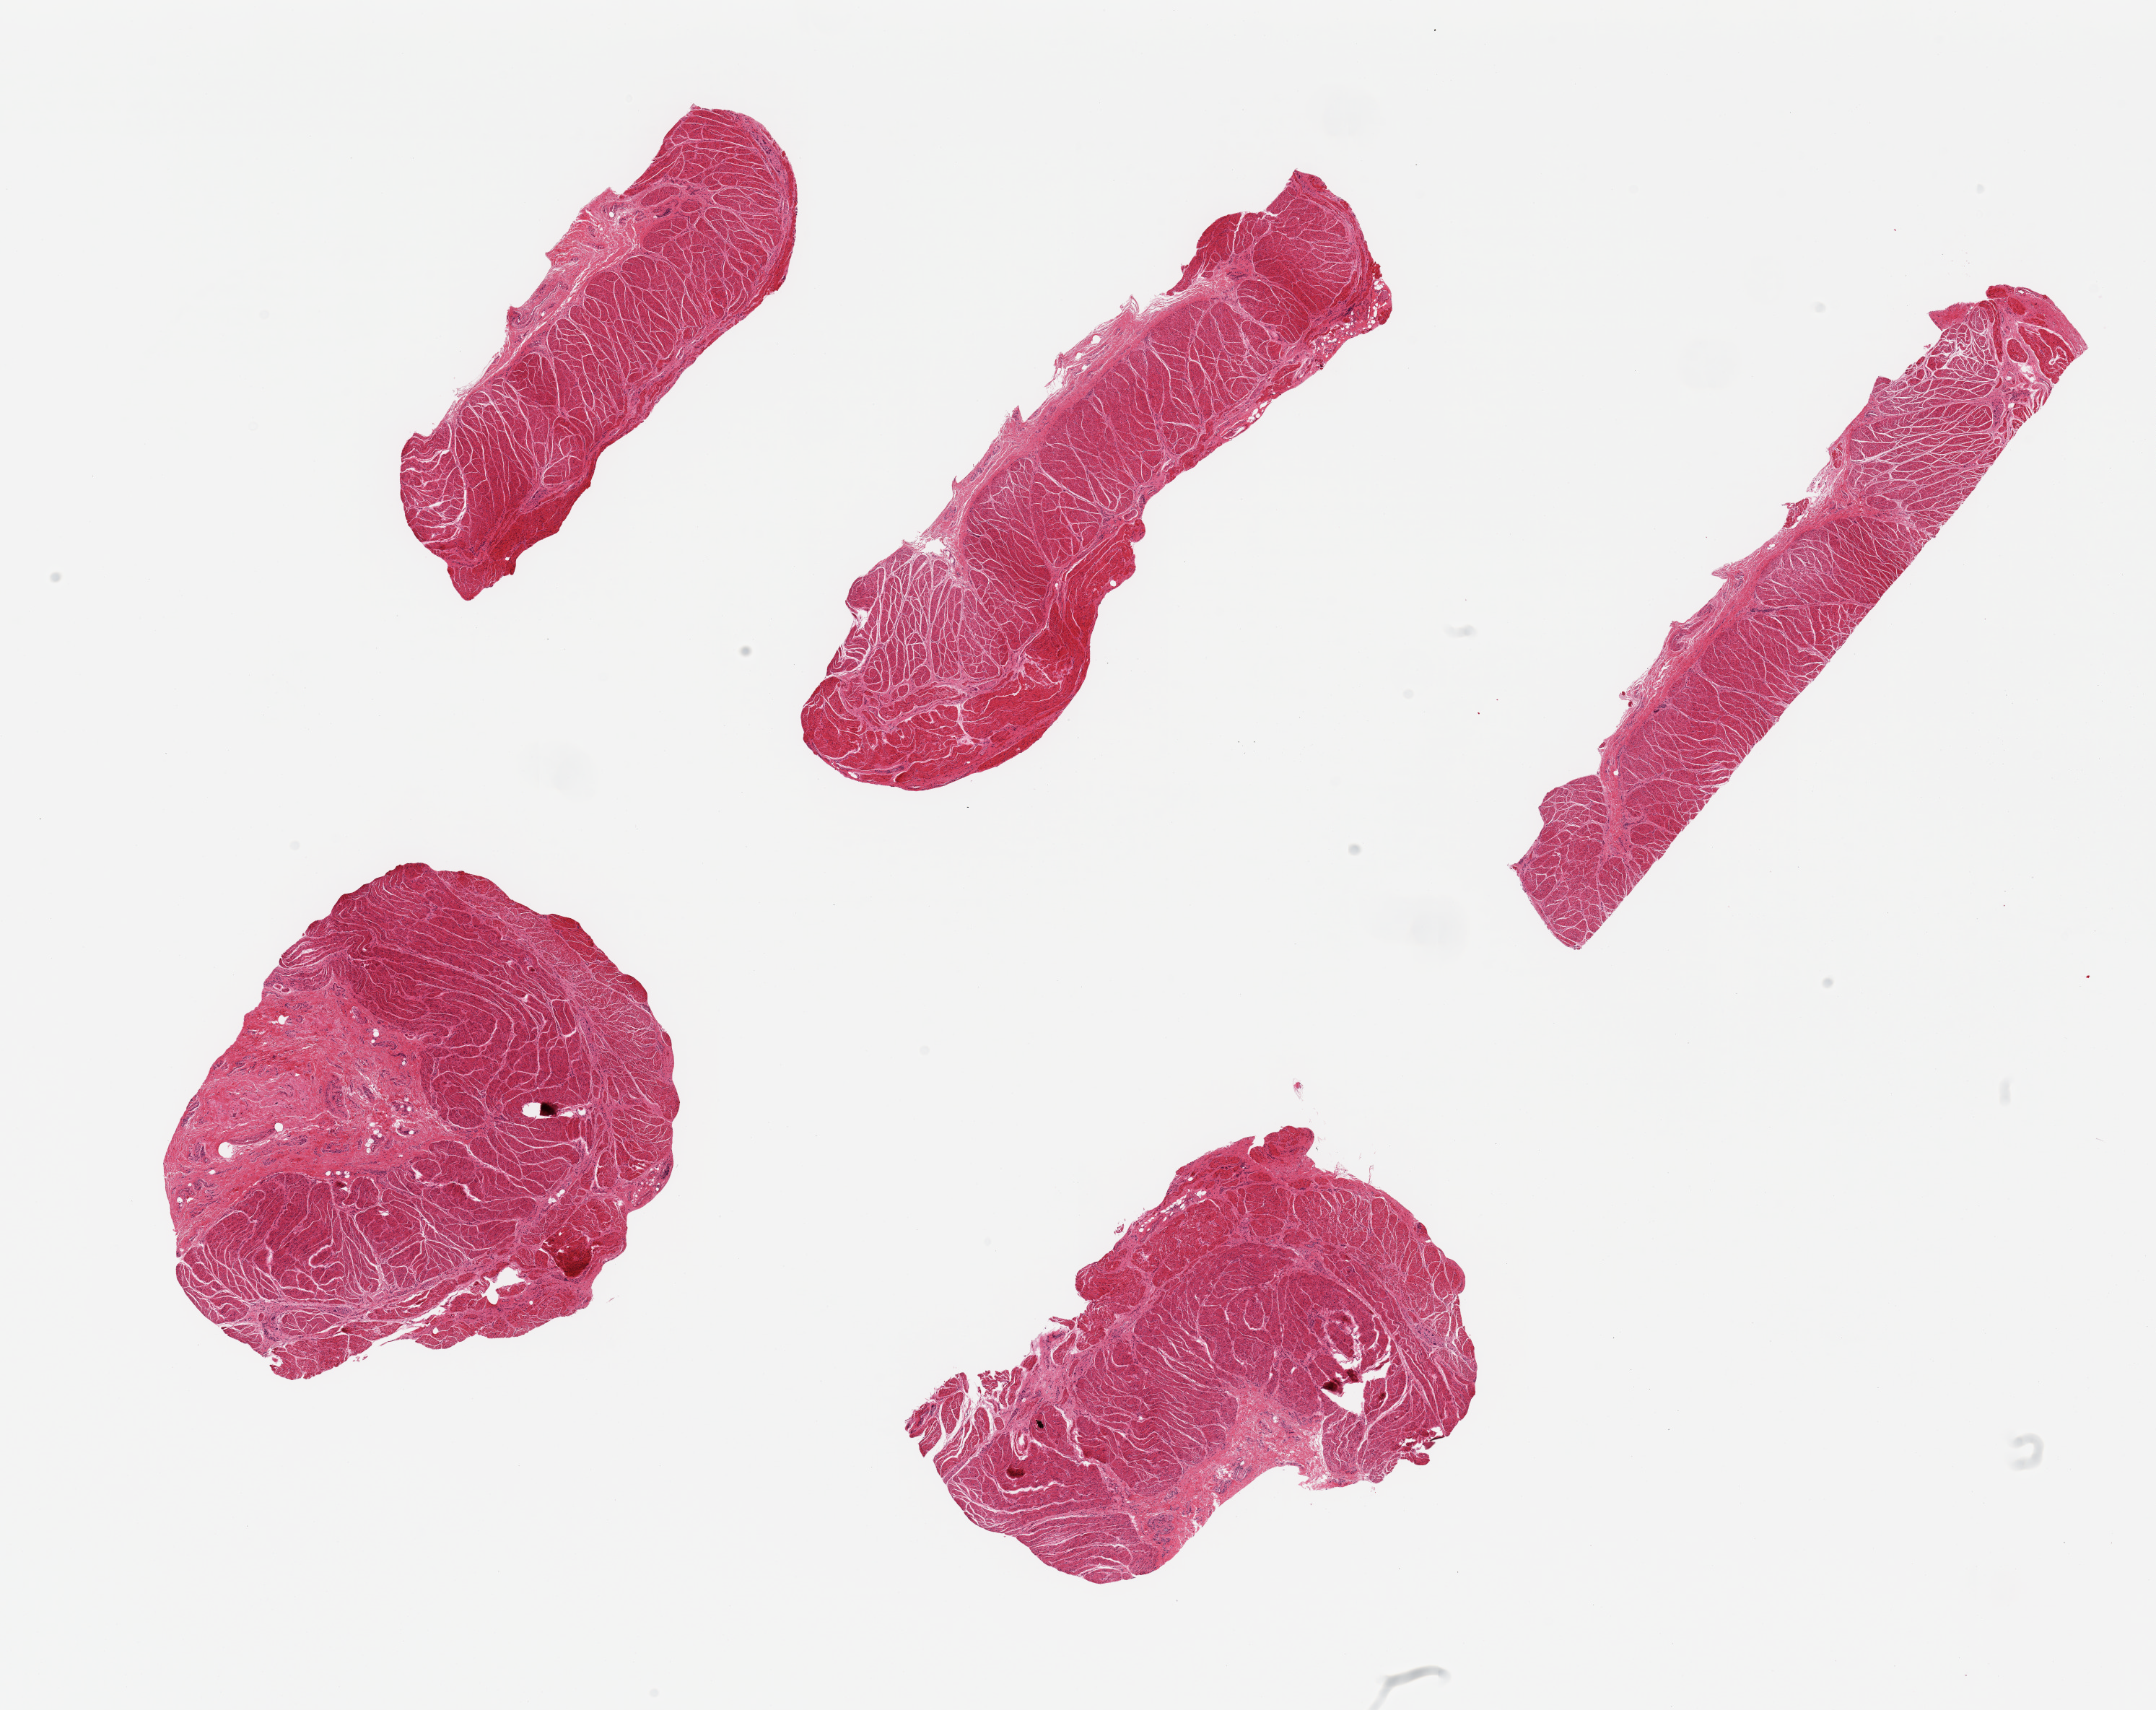
Whole-slide image, hematoxylin and eosin (H&E) stain — a low-resolution overview of the entire scanned area, about 23.6 x 18.7 mm. PAXgene-fixed, paraffin-embedded tissue. Section of gastroesophageal junction (target tissue). Donor tissue sample. Donor sex: male.
Reviewer comment on this tissue sample: 5 pieces; well trimmed.